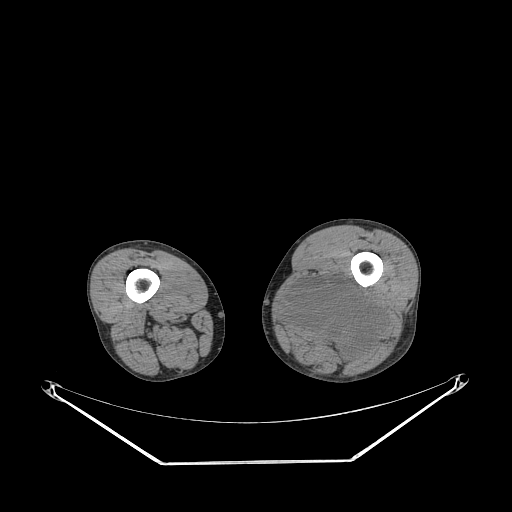
CT of an extremity soft-tissue mass (from a PET/CT study), one axial slice. Slice 218 of 267 in the series (ordered by position). Soft-tissue window (W 400 / L 40 HU). 512 × 512 image matrix, field of view 500 × 500 mm. Male patient. From the clinical record (not read from this slice): histological type: undifferentiated pleomorphic liposarcoma; grade: high; site of the primary tumour: left thigh.
Outlined on this slice (expert contour drawn on MRI and transferred to this co-registered scan by the dataset authors):
- gross tumour volume including surrounding oedema: box from (x=283, y=276) to (x=385, y=359) px
- gross tumour volume (mass): (x=283, y=278)–(x=385, y=359)